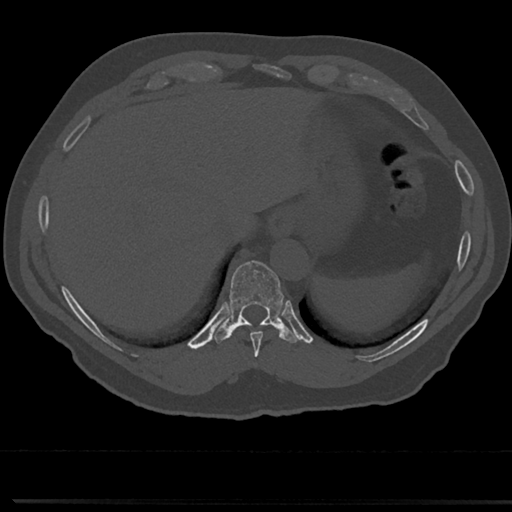
CT including the spine, one axial slice; slice 272 of 817 in the series (ordered by position); bone window (W 1800 / L 400 HU); 0.5 mm slice thickness; 512 × 512 image matrix, field of view 355 × 355 mm. Patient: male, 61 years. From the clinical record (not read from this slice): primary cancer: prostate.
Outlined on this slice (semi-automatically segmented with operator editing):
- T10 vertebra: bounding box (x1, y1, x2, y2) in pixels: (229, 261, 282, 324)
- T9 vertebra: (235, 322, 281, 352)